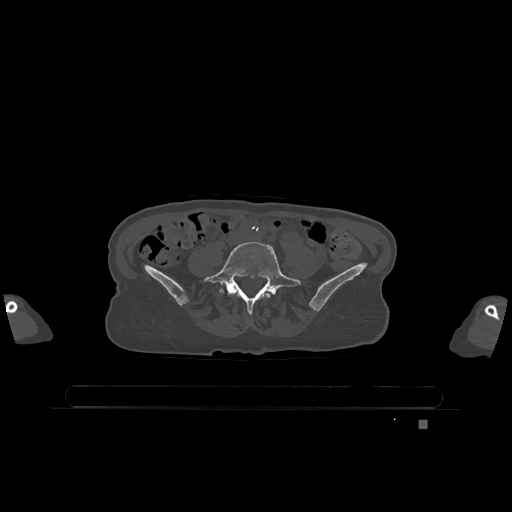
CT including the spine, one axial slice. Position 247 of 1317 along the scan axis. Bone window (W 1800 / L 400 HU). 0.5 mm slice thickness. 512 × 512 image matrix. Patient: female, 74 years. Case-level facts recorded for this patient, not image findings: primary cancer: lung; vertebrae with lytic lesions (as recorded): T1, T4, T5, T6, L4, L5.
Outlined on this slice (semi-automatically segmented with operator editing):
- L4 vertebra: box from (x=264, y=293) to (x=270, y=298) px
- L5 vertebra: (x=204, y=242)–(x=301, y=314)